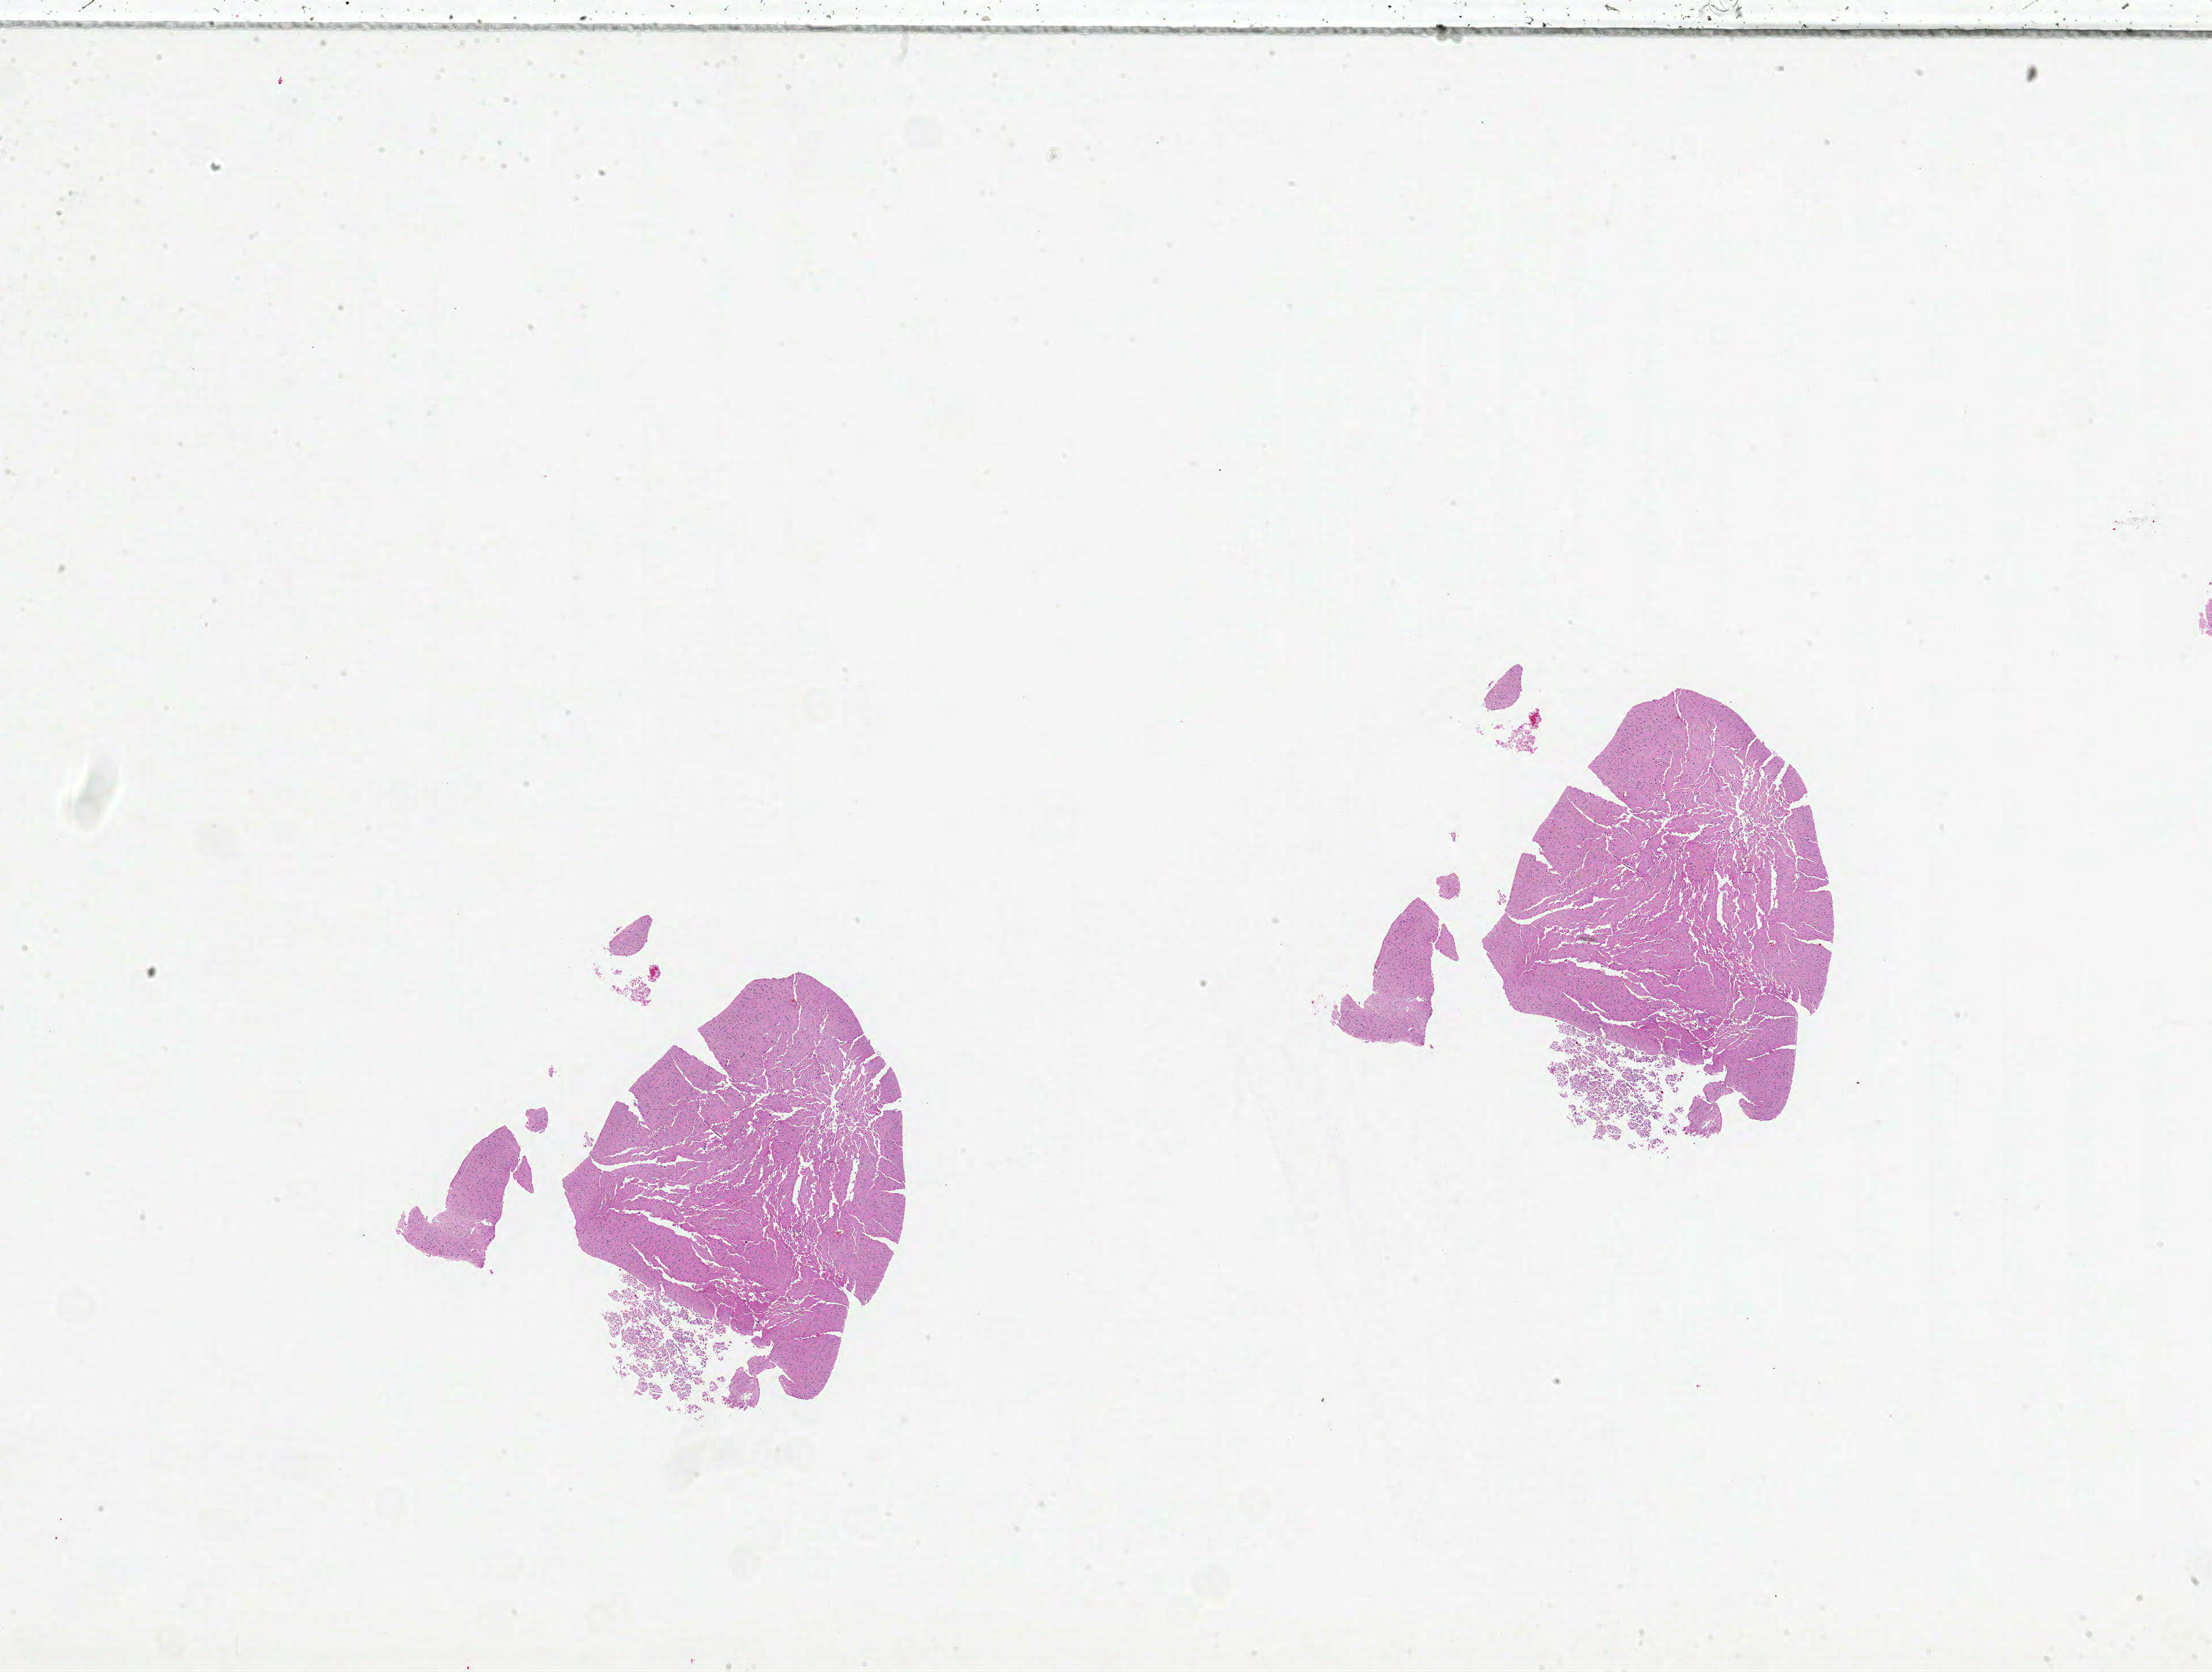
H&E whole-slide image — whole scanned area (about 31.0 x 23.4 mm) shown as a low-resolution overview, formalin-fixed paraffin-embedded (FFPE) diagnostic section, sample: primary tumour, brain. Patient: female, age at initial diagnosis 47 years.
* pathologic diagnosis: Glioblastoma